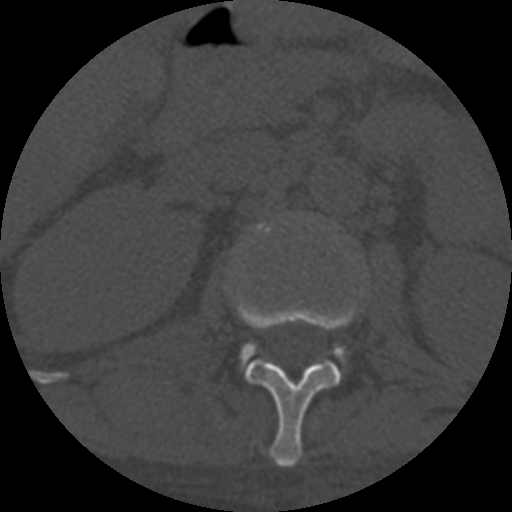
CT including the spine, one axial slice; slice 277 of 708 in the series (ordered by position); reconstruction kernel STANDARD; 120 kVp; one of 3 acquisitions stored at this slice position; bone window (W 1800 / L 400 HU); 1.25 mm slice thickness; 512 × 512 image matrix, field of view 160 × 160 mm. Patient age 55 years. Case-level facts recorded for this patient, not image findings: primary cancer: colon; vertebrae with lytic lesions (as recorded): T12, L1, L5.
Annotated regions visible in this slice (semi-automatic segmentation, software-assisted and operator-edited):
- L1 vertebra: box from (x=234, y=294) to (x=355, y=467) px
- L2 vertebra: (x=243, y=225)–(x=345, y=361)